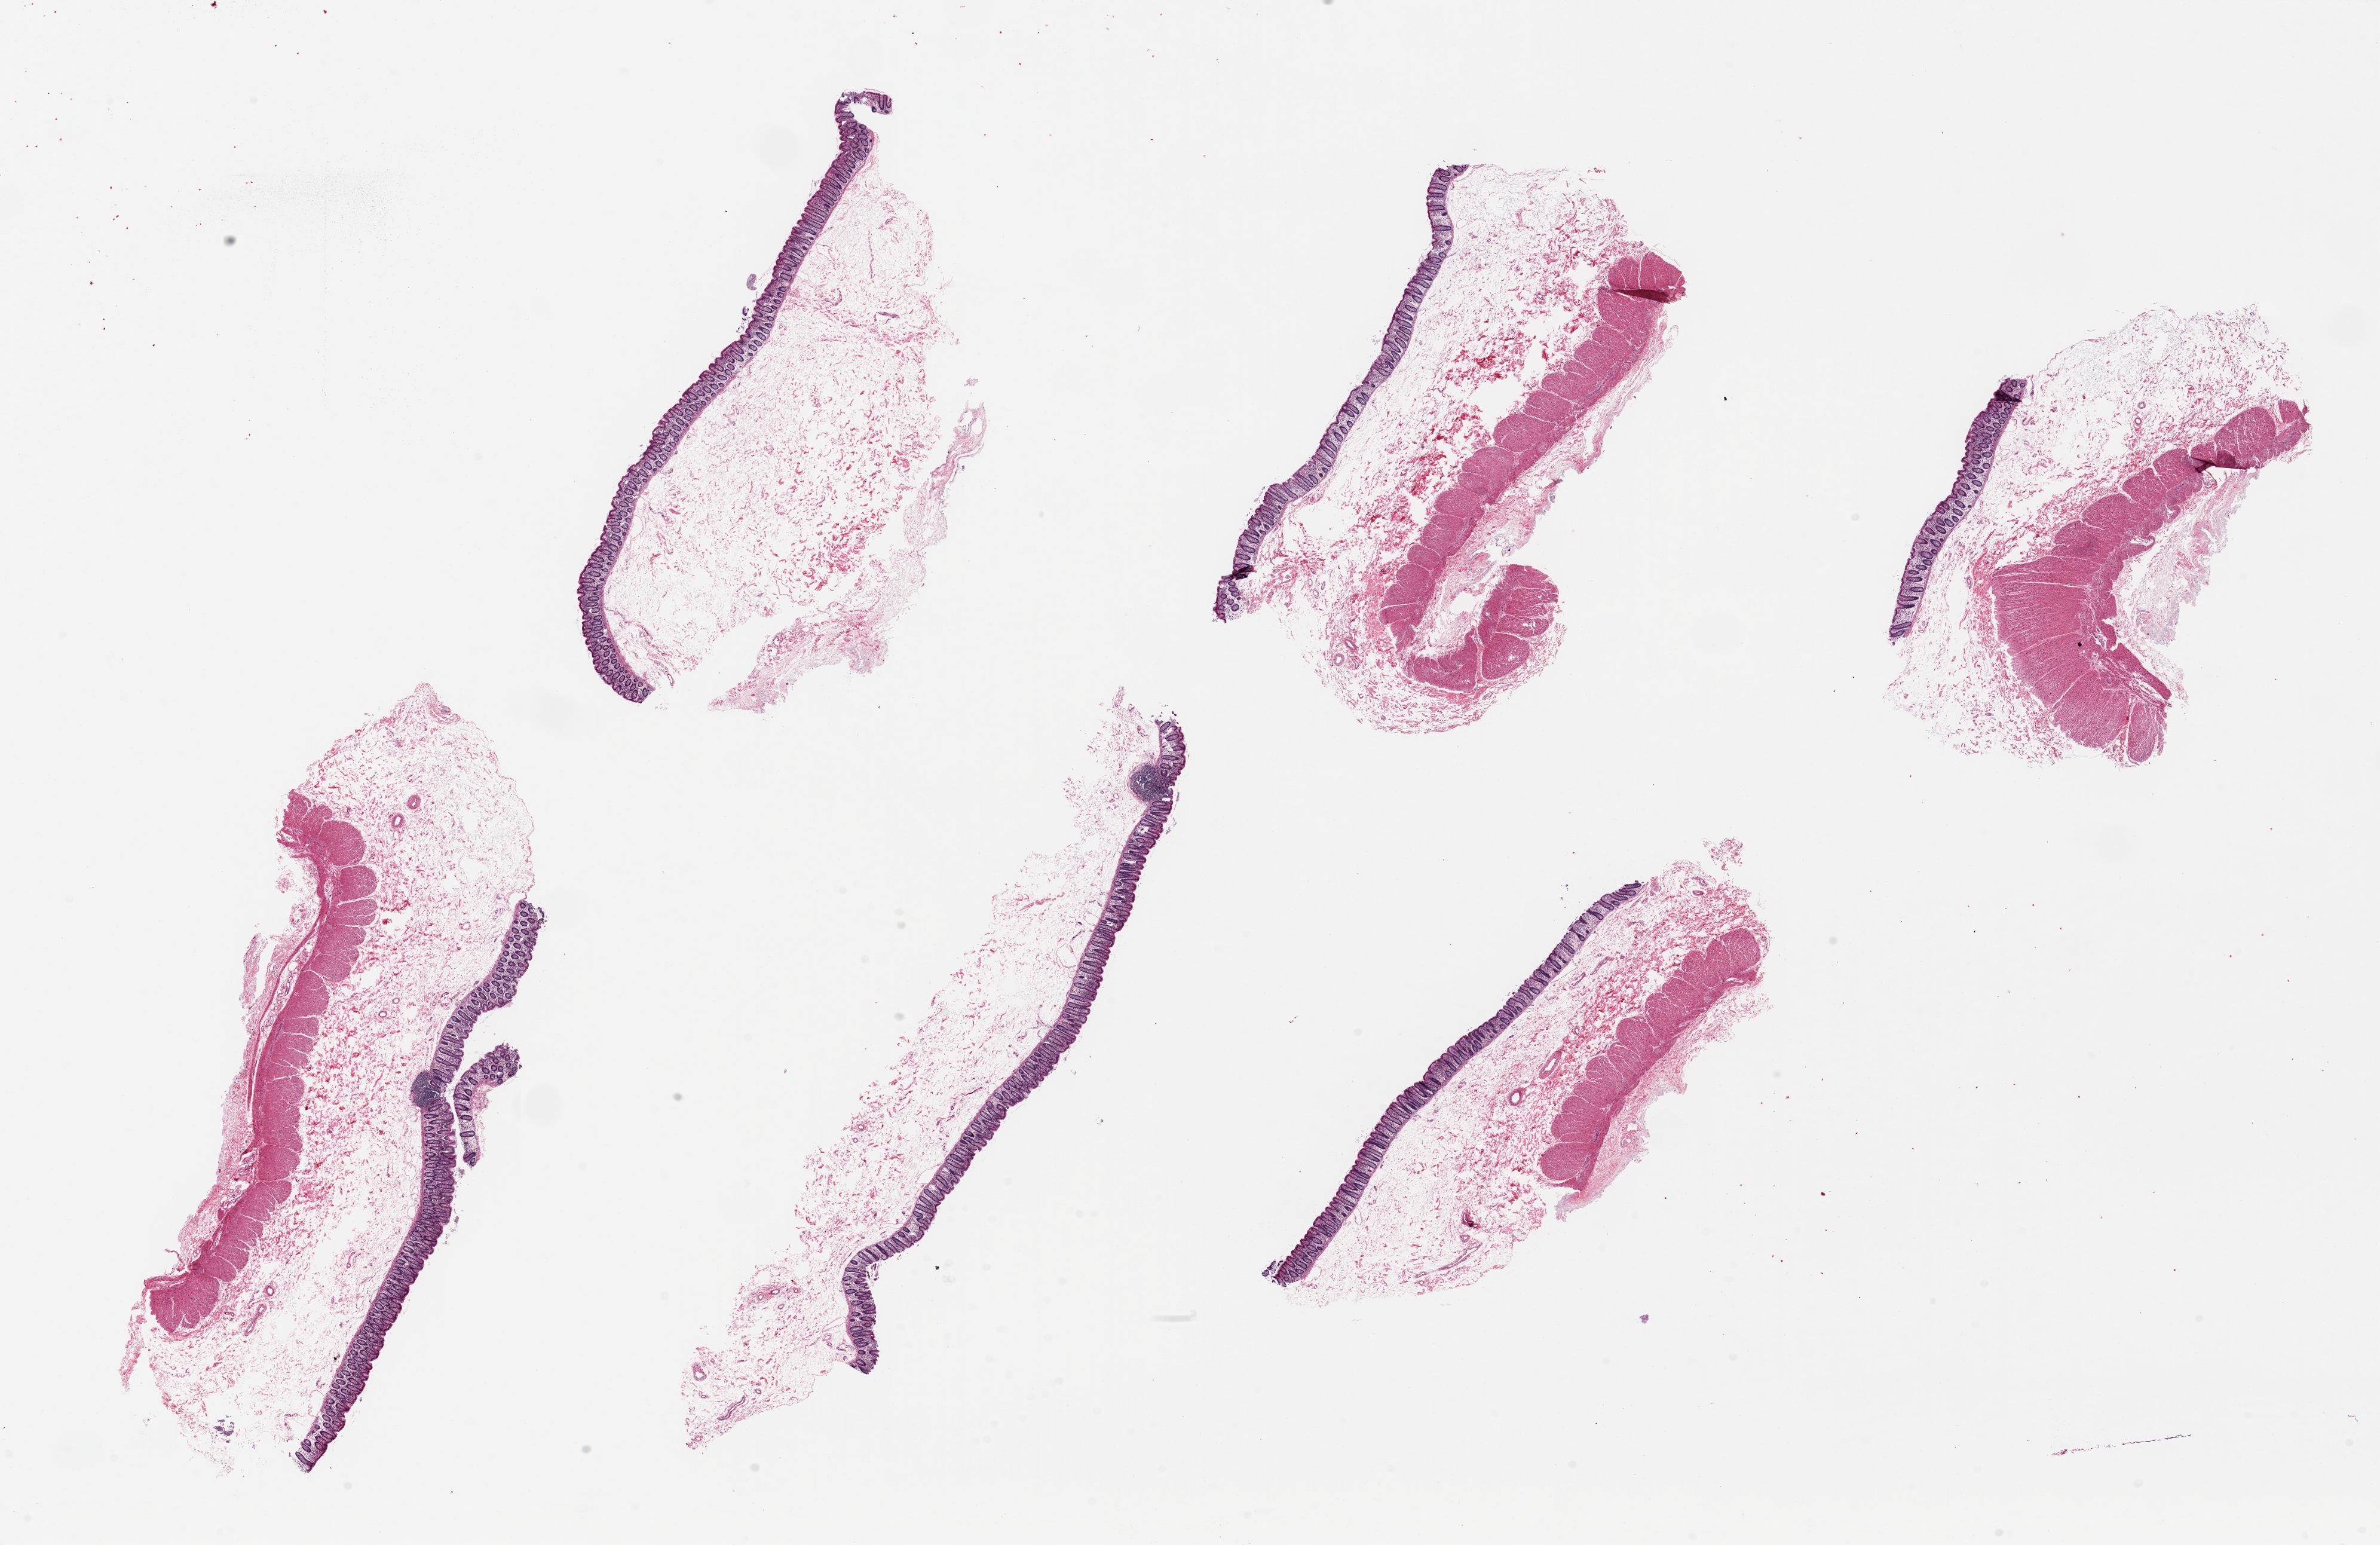
Digitized H&E-stained section, shown as a low-resolution overview of the whole scanned area (about 31.5 x 20.4 mm), PAXgene-fixed paraffin-embedded (PFPE) section, target tissue: transverse colon, donor tissue sample. Male donor.
Reviewer comment on this tissue sample: 6 pieces ~9x3mm. Mucosa remarkably well-preserved, ~10% of thickness.